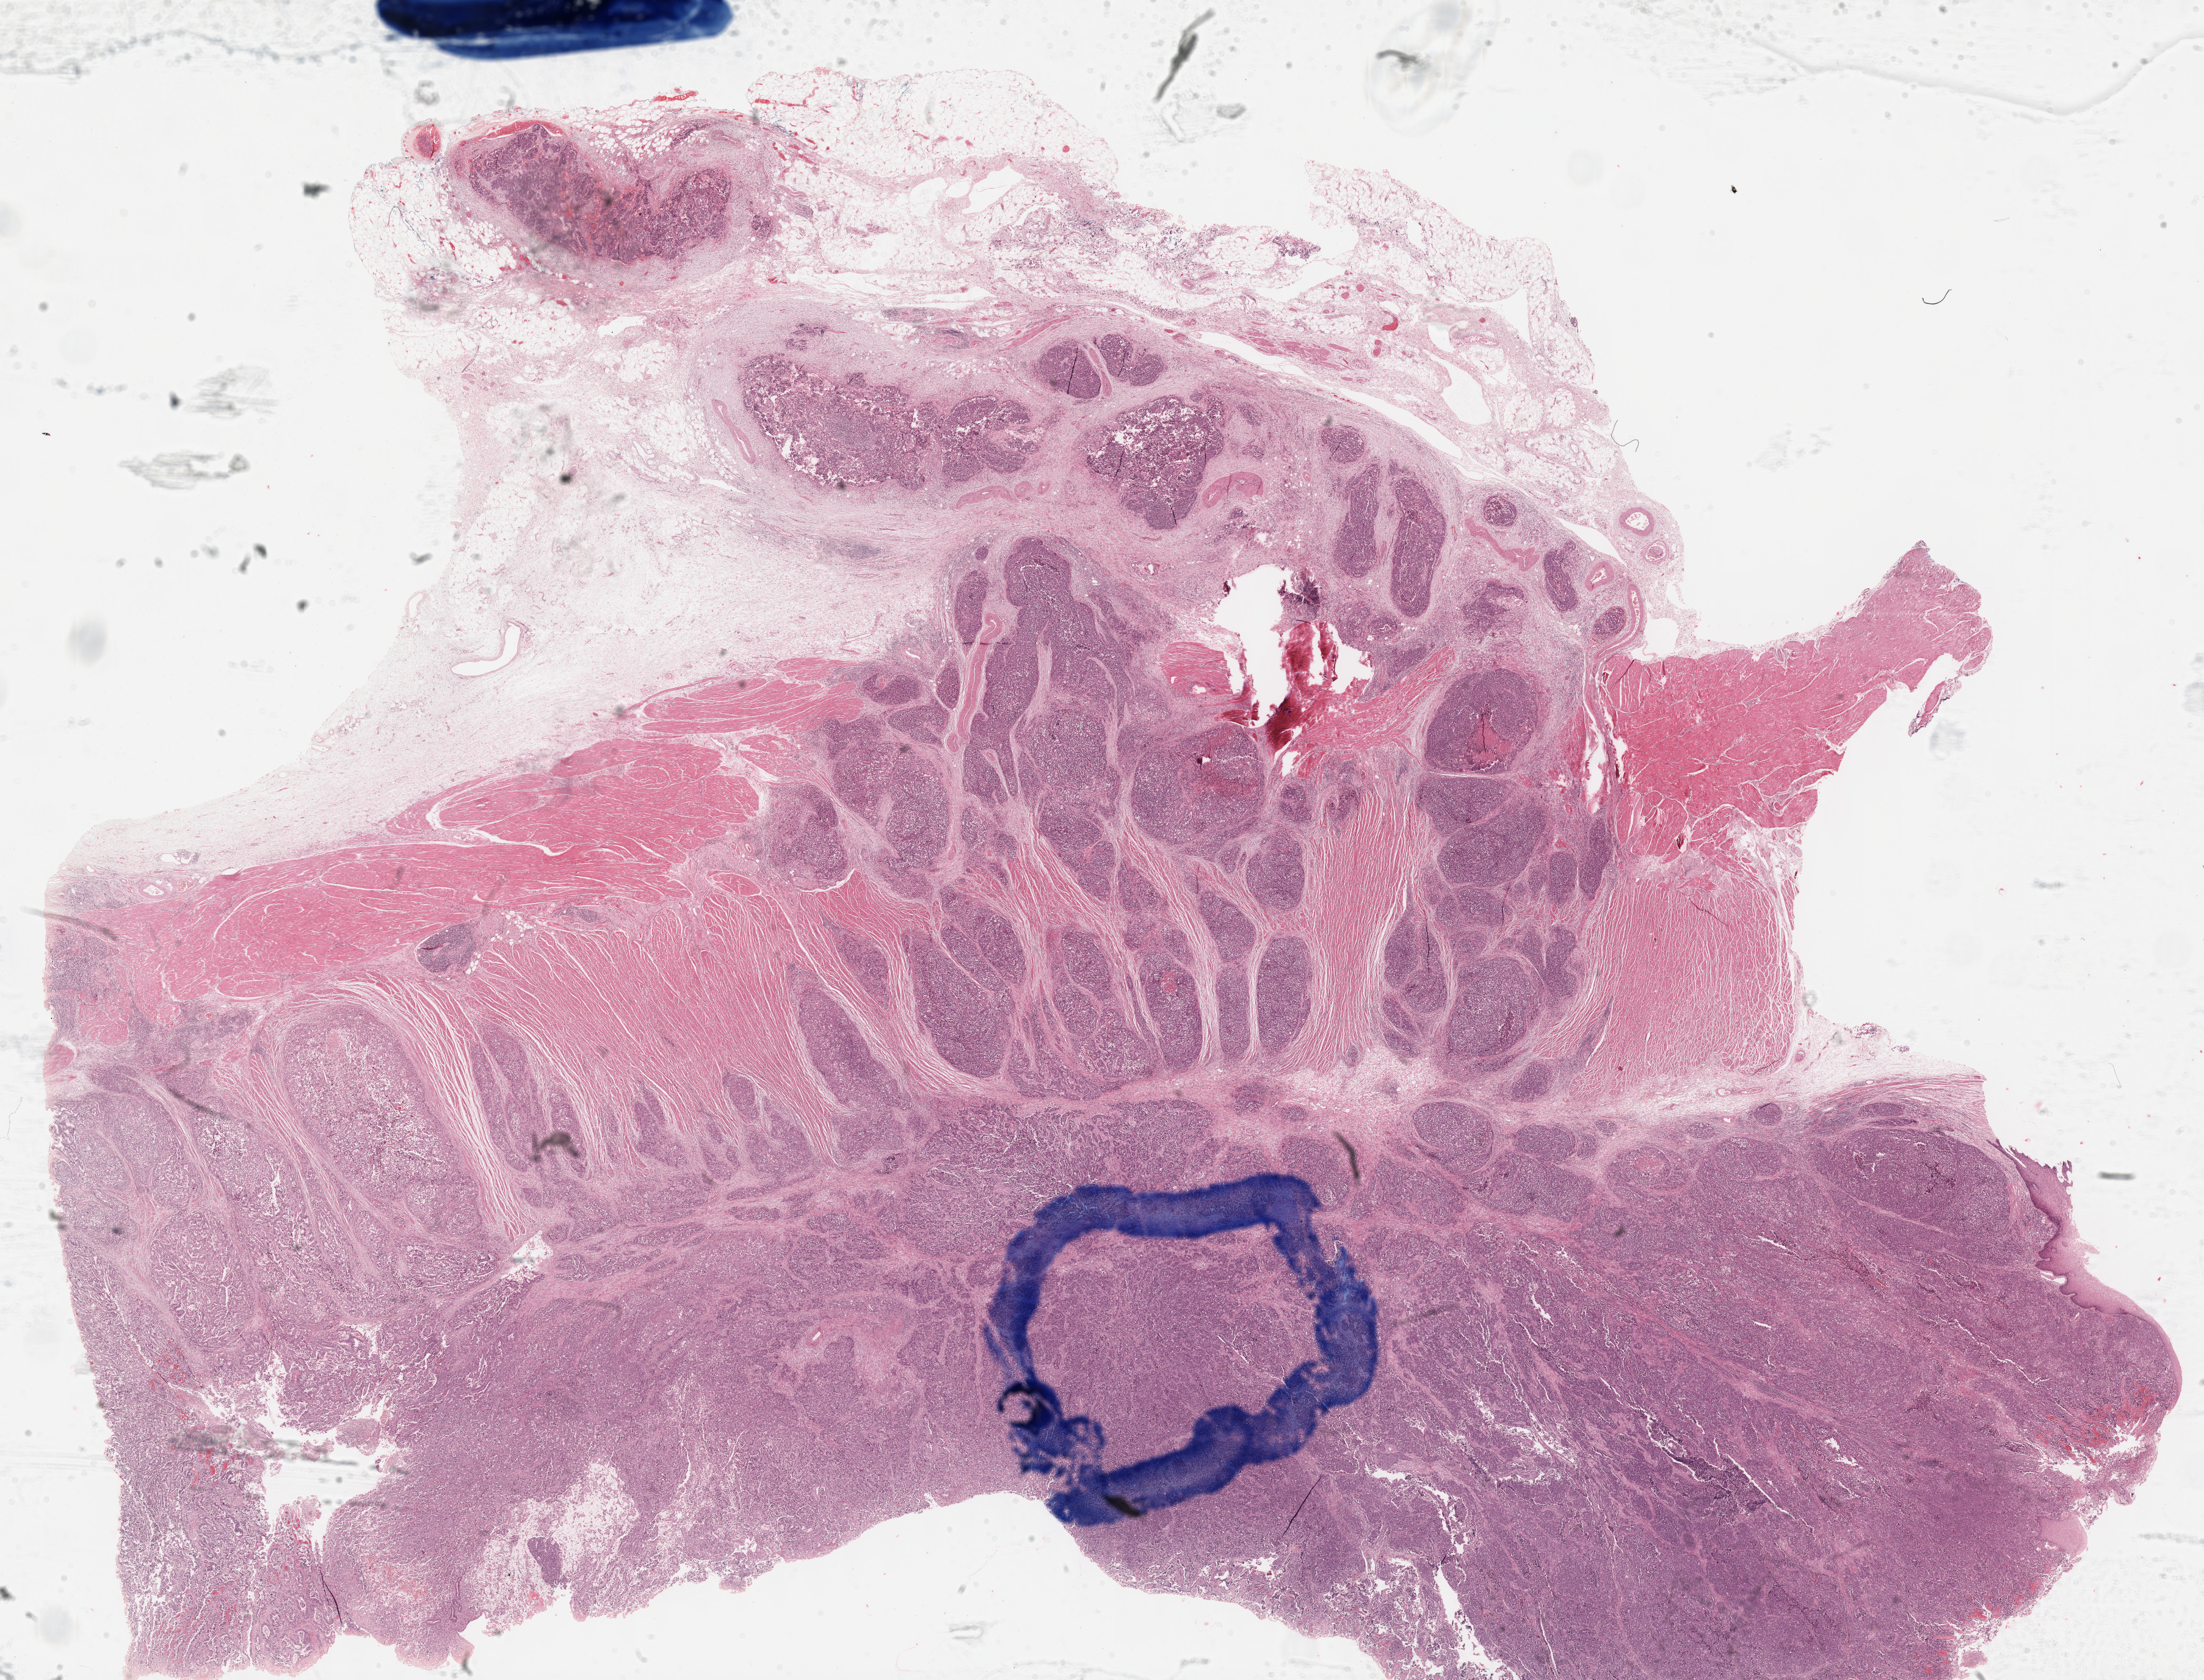
Hematoxylin and eosin (H&E) stained whole-slide image — a low-resolution overview of the entire scanned area, about 29.2 x 22.2 mm (acquisition: 40x scan); formalin-fixed paraffin-embedded (FFPE) diagnostic section; esophagus, primary tumour sample. Male patient; age at initial diagnosis 70 years. Histologic grade: G3 (poorly differentiated).
TNM: T3 N1 M0. AJCC pathologic stage: III (5th edition). Pathologic diagnosis: Adenocarcinoma, NOS (lower third of esophagus).